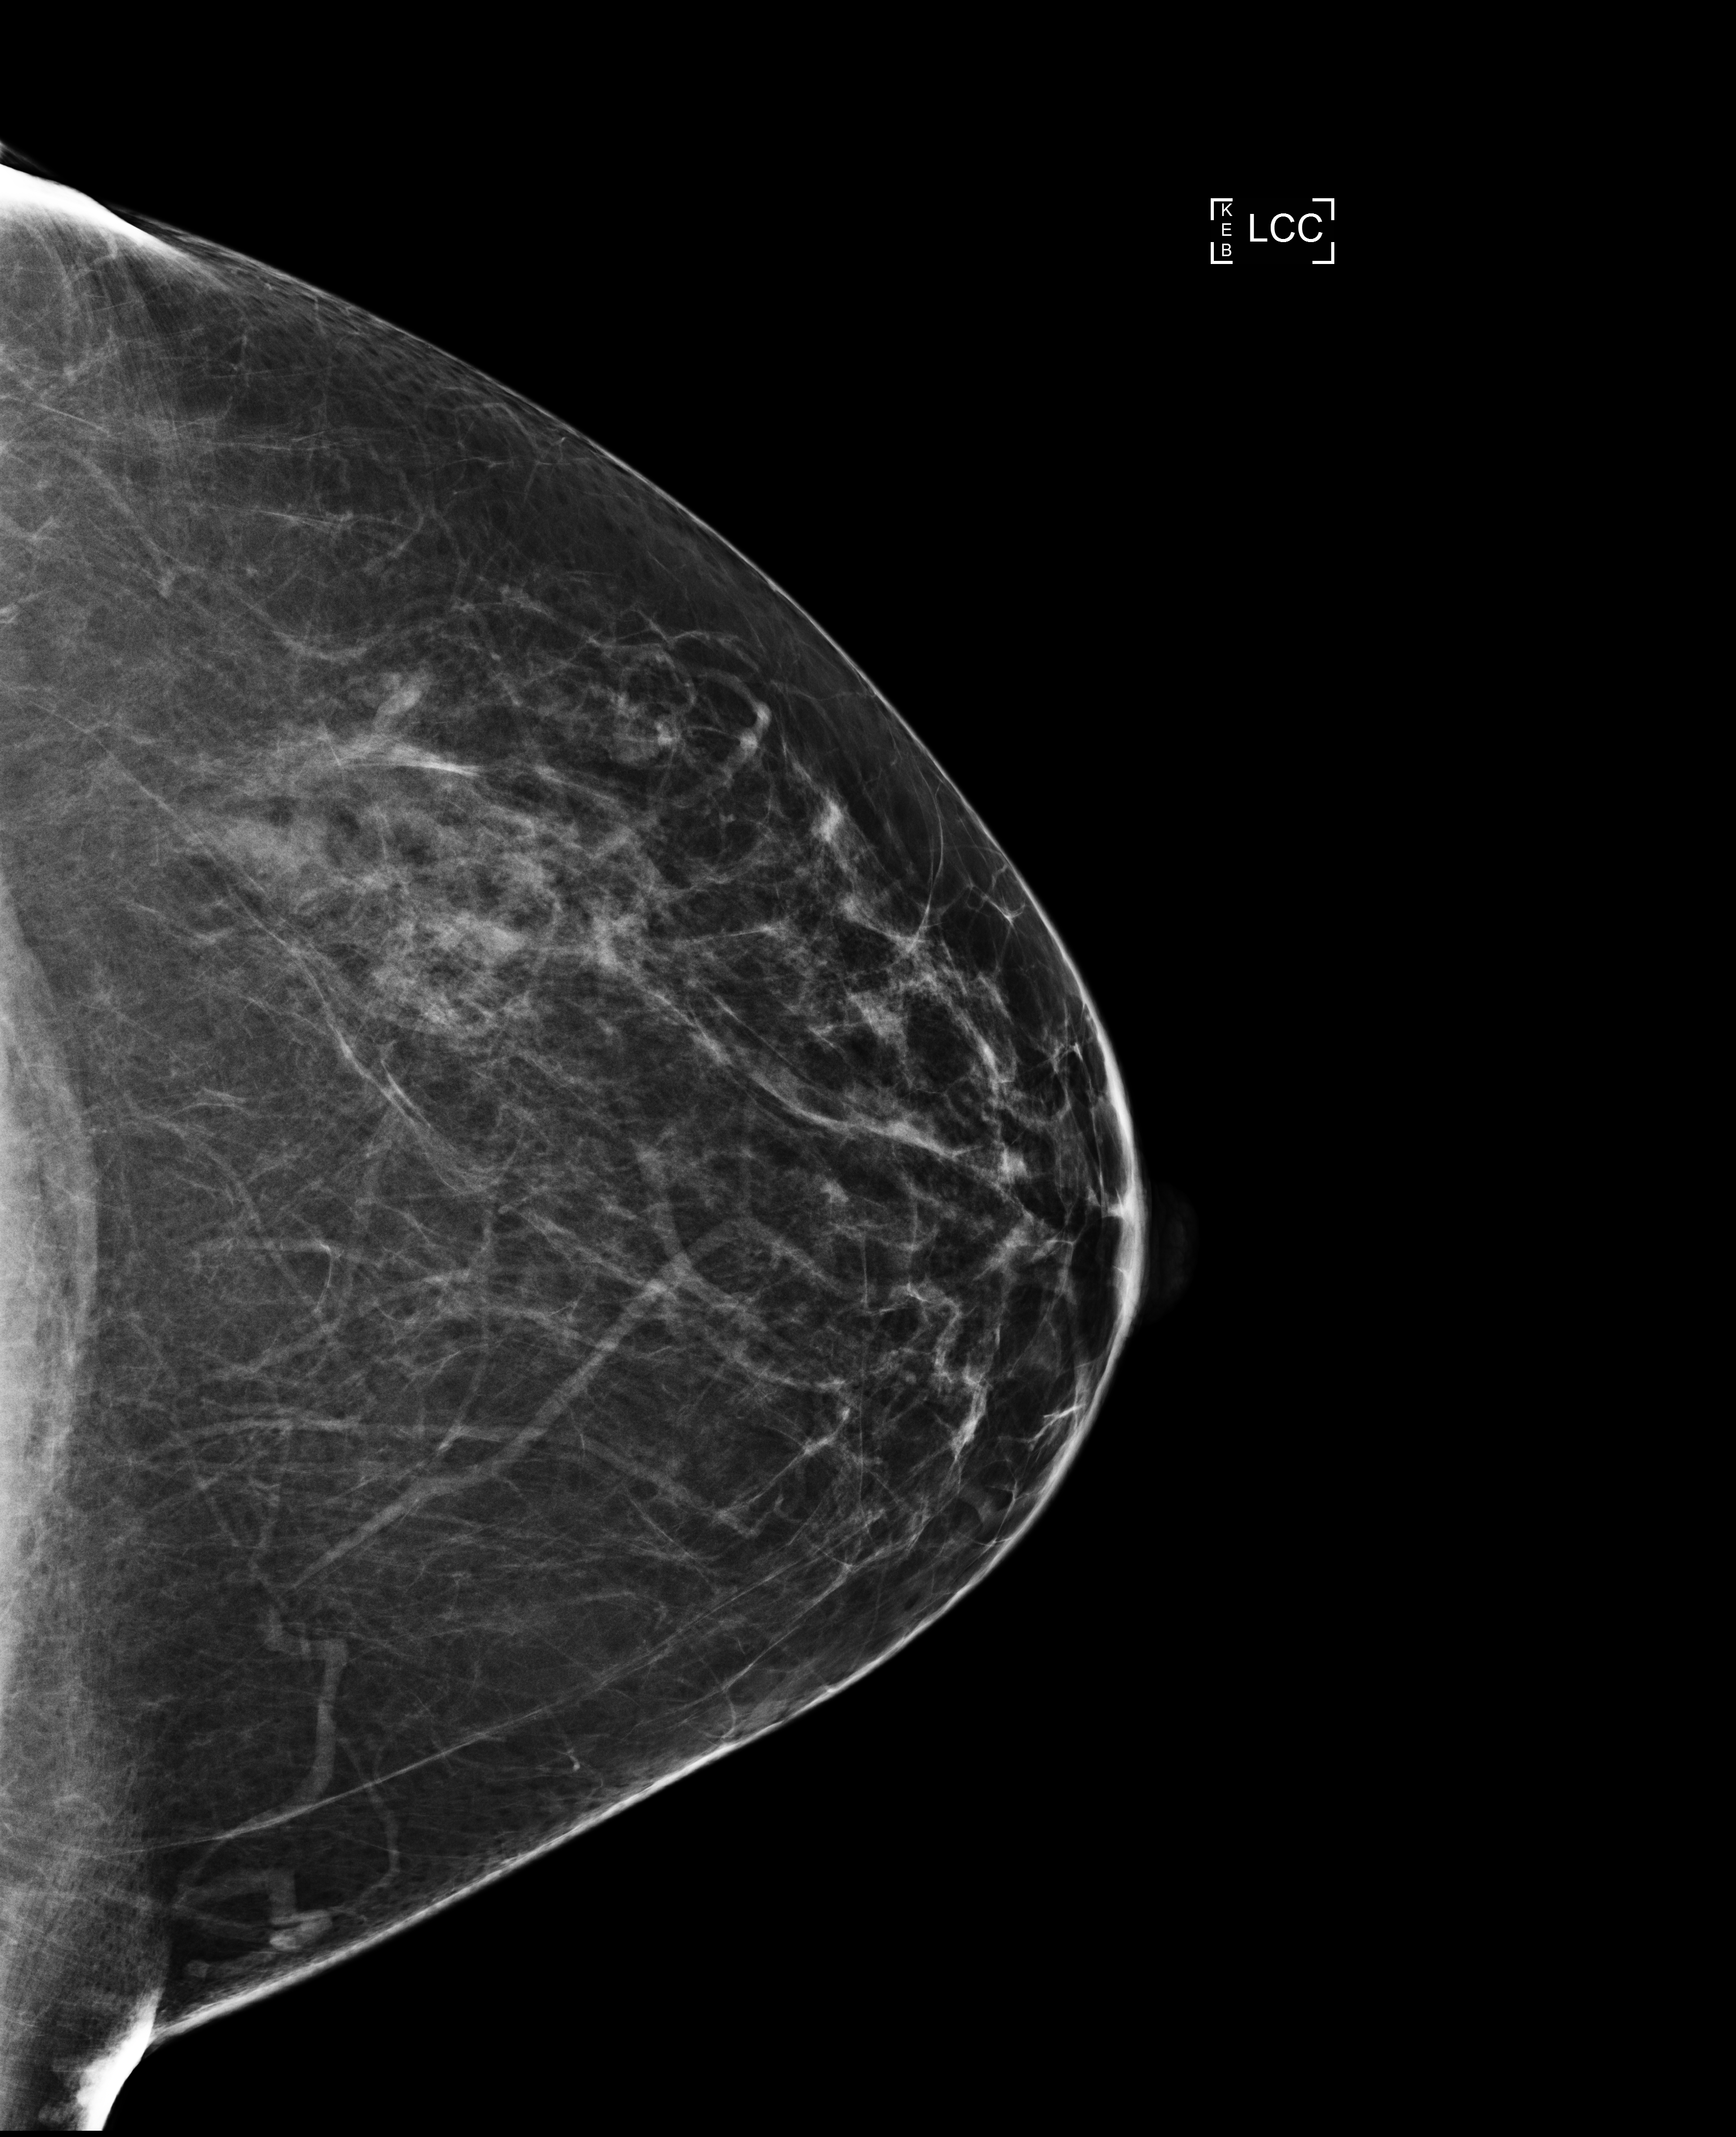
Annual screening mammography examination; compressed breast thickness 76 mm; system: Selenia Dimensions. Patient aged 53 years (female).
Image type: full-field digital mammogram. Breast: left. Projection: CC view.